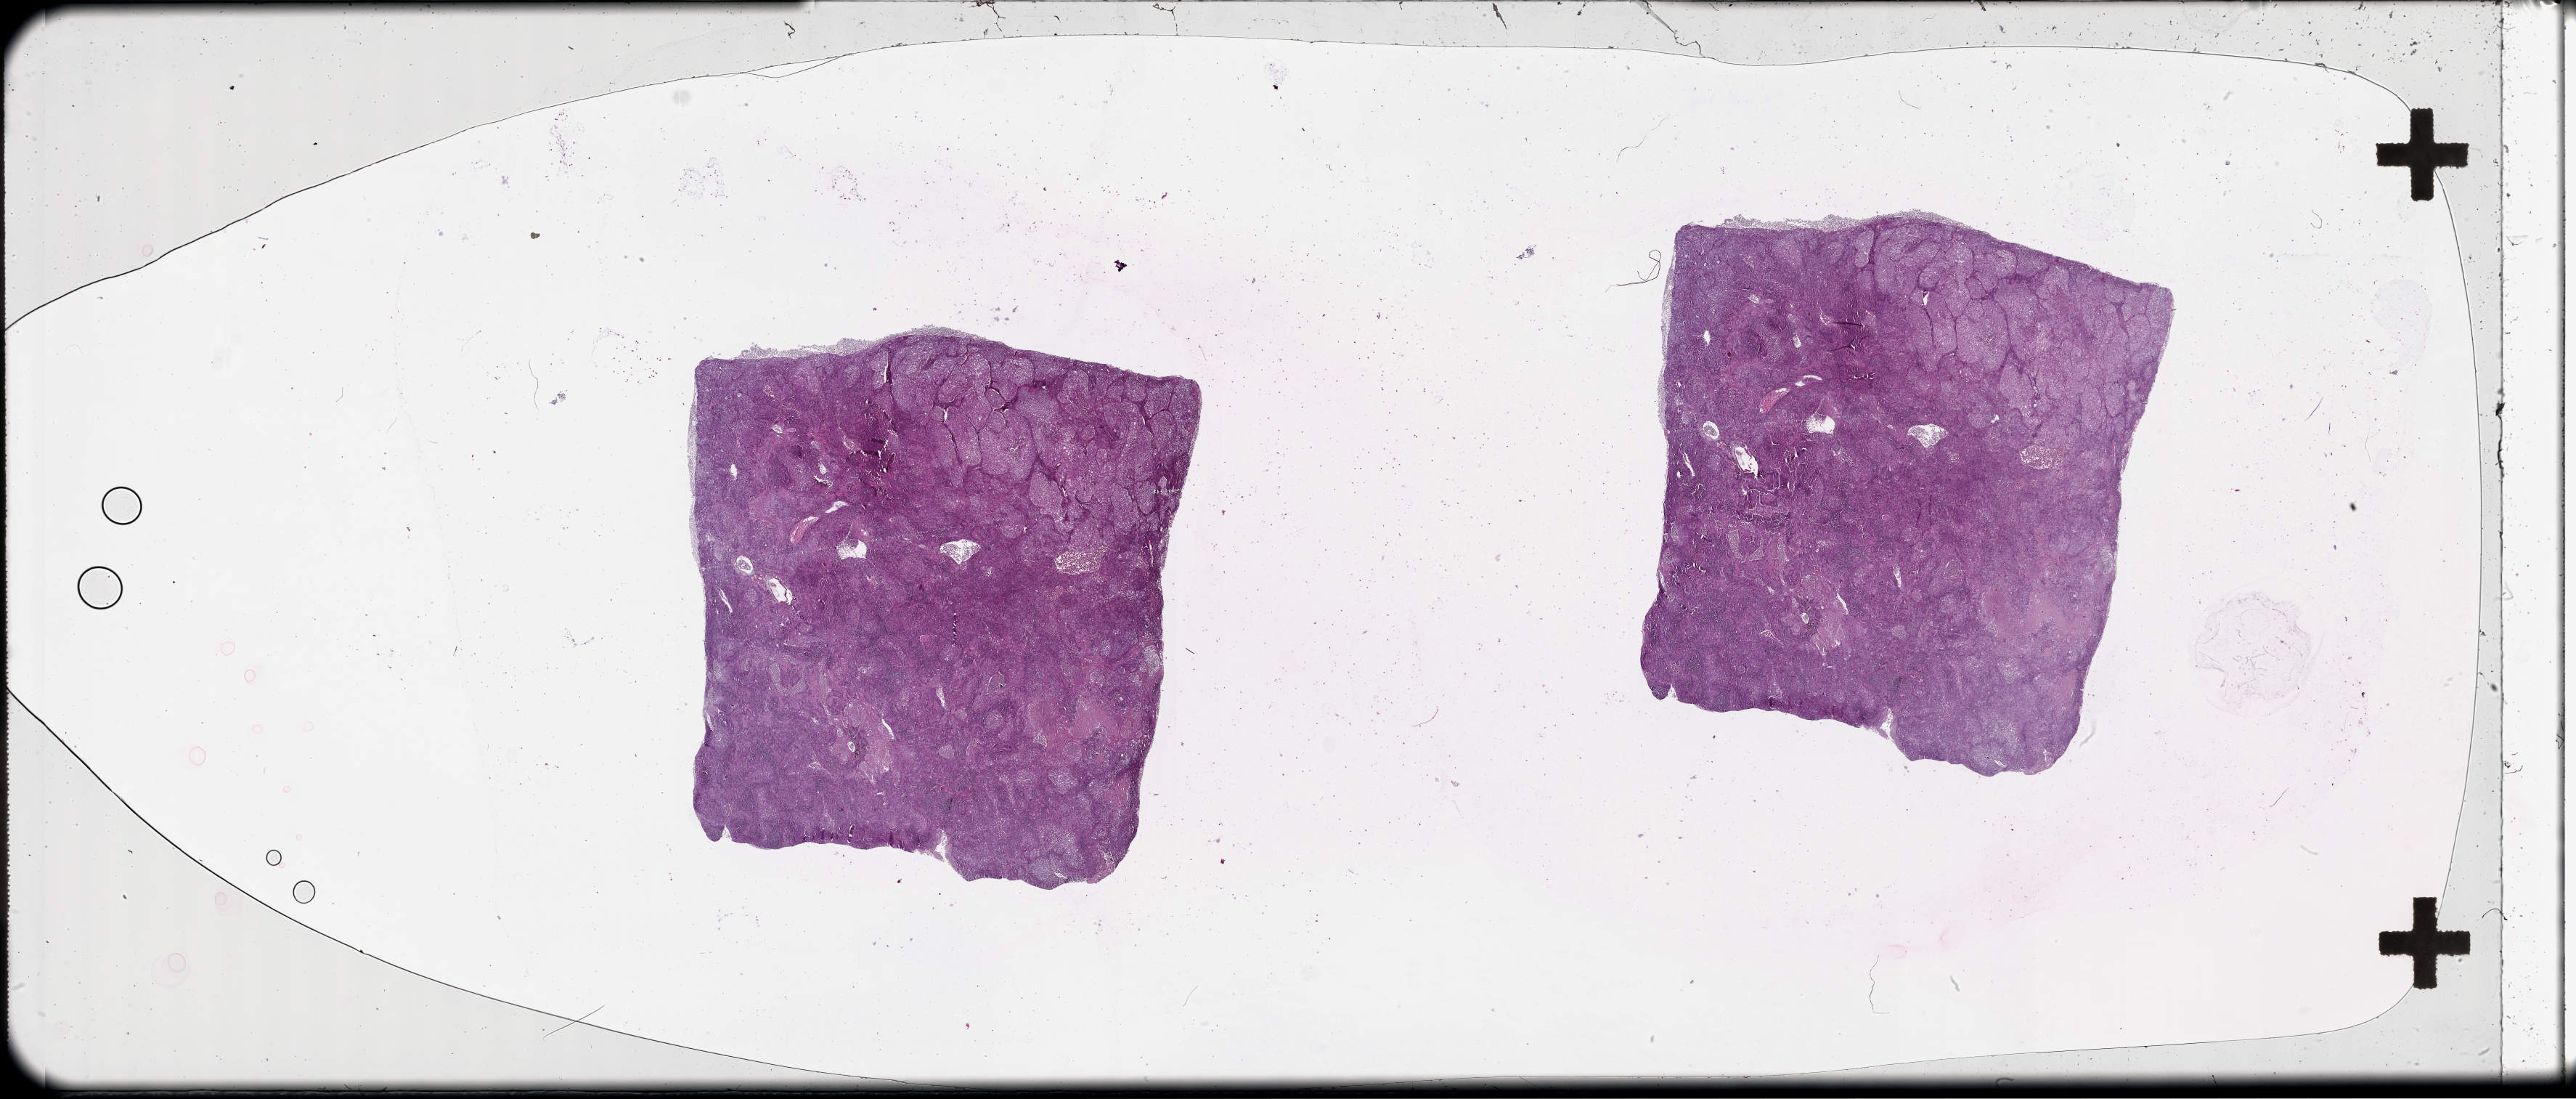
H&E whole-slide image, whole scanned area (about 57.1 x 24.4 mm, acquisition: 20x scan) shown as a low-resolution overview; tumour tissue sample, lung. 72-year-old female patient.
* patient diagnosis (cohort enrolment): squamous cell carcinoma (lung)